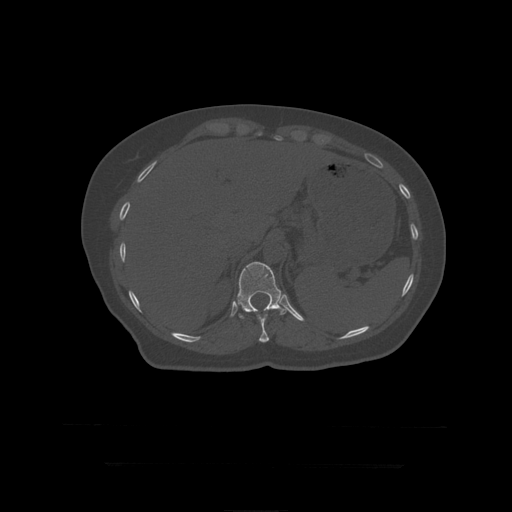
CT including the spine, one axial slice. Slice 206 of 399 in the series (ordered by position). 120 kVp. Bone window (W 1800 / L 400 HU). 1.25 mm slice thickness. 512 × 512 image matrix. Patient age 41 years. From the clinical record (not read from this slice): primary cancer: breast.
Outlined on this slice (semi-automatically segmented with operator editing):
- T11 vertebra: bounding box (x1, y1, x2, y2) in pixels: (247, 312, 270, 343)
- T12 vertebra: (237, 262, 289, 319)